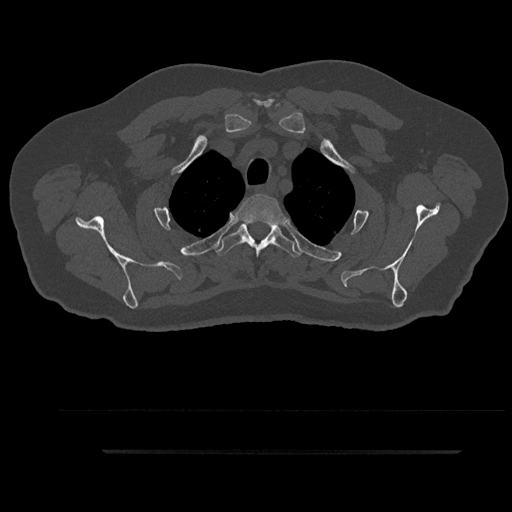
CT including the spine, one axial slice; slice 734 of 797 in the series (ordered by position); 120 kVp; bone window (W 1800 / L 400 HU); 0.5 mm slice thickness; 512 × 512 image matrix, field of view 432 × 432 mm. Male patient, age 63 years. From the clinical record (not read from this slice): primary cancer: renal; vertebrae with lytic lesions (as recorded): T8.
Outlined on this slice (semi-automatically segmented with operator editing):
- T2 vertebra: bounding box (x1, y1, x2, y2) in pixels: (237, 194, 285, 241)
- T3 vertebra: (215, 222, 302, 259)